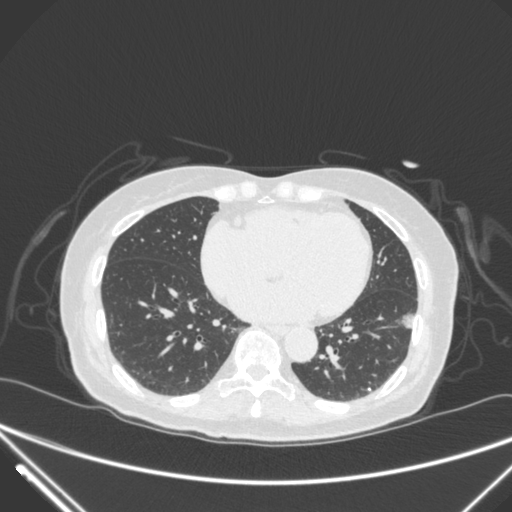
Chest CT, one axial slice. Slice 116 of 310 in the series (ordered by position). Lung window (W 1500 / L -600 HU). 1 mm slice thickness. 512 × 512 image matrix, field of view 377 × 377 mm. Patient: female, 82 years. From the clinical record (not read from this slice): clinical TNM (as recorded): T1c N0 M0; histopathological grade: G2.
Outlined on this slice (bounding box drawn by a radiologist):
- lung tumour (recorded histology: adenocarcinoma): bounding box (x1, y1, x2, y2) in pixels: (387, 304, 420, 345)